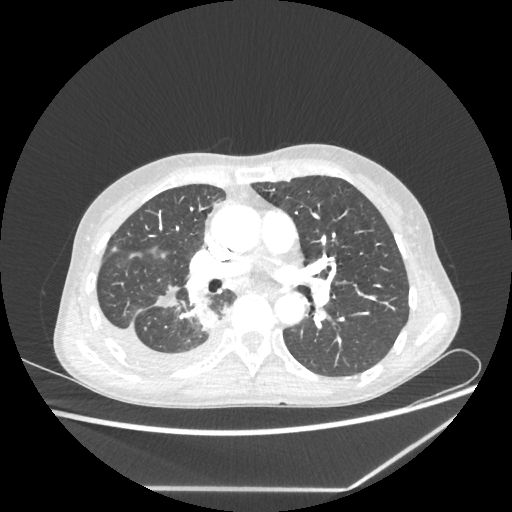
Chest CT, one axial slice. Slice 129 of 237 in the series (ordered by position). Lung window (W 1500 / L -600 HU). 512 × 512 image matrix. Female patient, age 59 years. From the clinical record (not read from this slice): clinical TNM (as recorded): T1c N1 M1.
Annotated regions visible in this slice (bounding box drawn by a radiologist):
- lung tumour (recorded histology: adenocarcinoma): bounding box (x1, y1, x2, y2) in pixels: (192, 305, 217, 334)